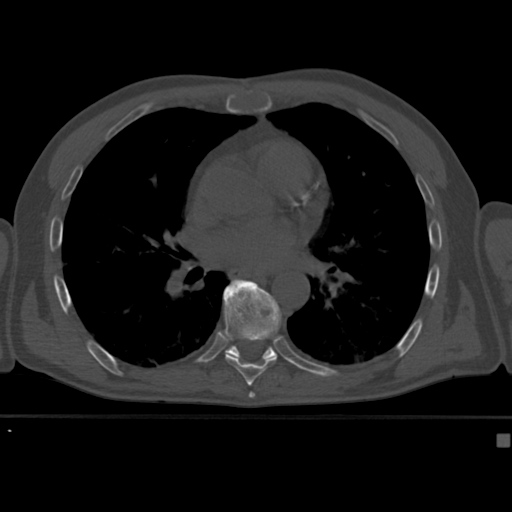
CT including the spine, one axial slice; slice 258 of 430 in the series (ordered by position); bone window (W 1800 / L 400 HU); 1.5 mm slice thickness; 512 × 512 image matrix. Male patient, age 64 years. Case-level facts recorded for this patient, not image findings: primary cancer: uterus; vertebrae with lytic lesions (as recorded): T1, T4, T5, T7, L5.
Outlined on this slice (semi-automatically segmented with operator editing):
- T8 vertebra: bounding box <222,279,282,382> (left, top, right, bottom; pixels)
- T9 vertebra: <225,281,279,374>